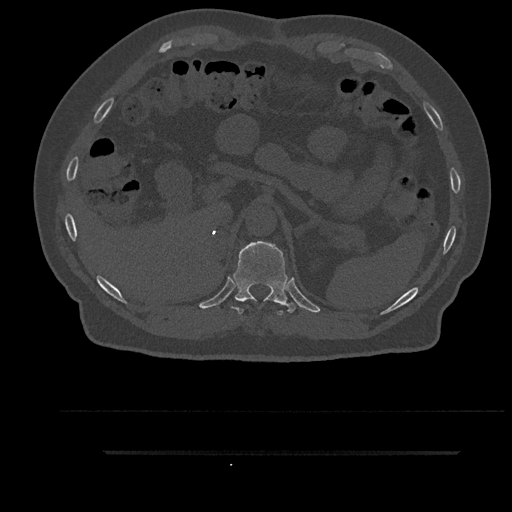
CT including the spine, one axial slice. 120 kVp. Bone window (W 1800 / L 400 HU). 512 × 512 image matrix, field of view 432 × 432 mm. Male patient, age 63 years. Case-level facts recorded for this patient, not image findings: primary cancer: renal; vertebrae with lytic lesions (as recorded): T8.
Annotated regions visible in this slice (semi-automatically segmented with operator editing):
- T11 vertebra: bounding box [x1, y1, x2, y2] px = [233, 241, 296, 315]